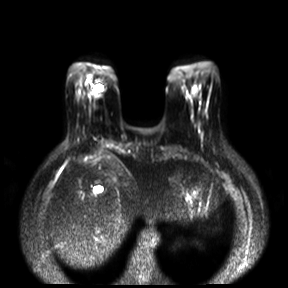
Breast MRI, one axial slice. Position 5 of 30 along the scan axis. Diffusion-weighted series; image 2 of 4 stored at this slice position (different b-values; order by instance number). 3 T. 4 mm slice thickness. 288 × 288 image matrix, field of view 360 × 360 mm. Female patient.
Annotated regions visible in this slice (expert manual segmentation):
- tumour on diffusion-weighted imaging: bounding box <187,91,195,98> (left, top, right, bottom; pixels)